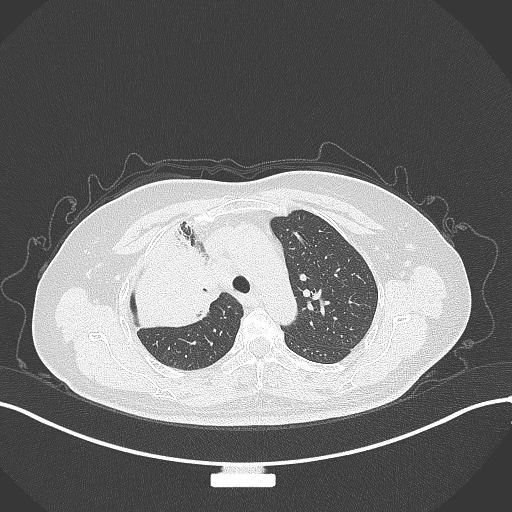
Chest CT, one axial slice; position 225 of 309 along the scan axis; reconstruction kernel B70f; 120 kVp; lung window (W 1500 / L -600 HU); 1 mm slice thickness; 512 × 512 image matrix, field of view 400 × 400 mm. Female patient, age 60 years. From the clinical record (not read from this slice): clinical TNM (as recorded): T3 N1 M1.
Annotated regions visible in this slice (bounding box drawn by a radiologist):
- lung tumour (recorded histology: adenocarcinoma): box from (x=128, y=222) to (x=222, y=336) px